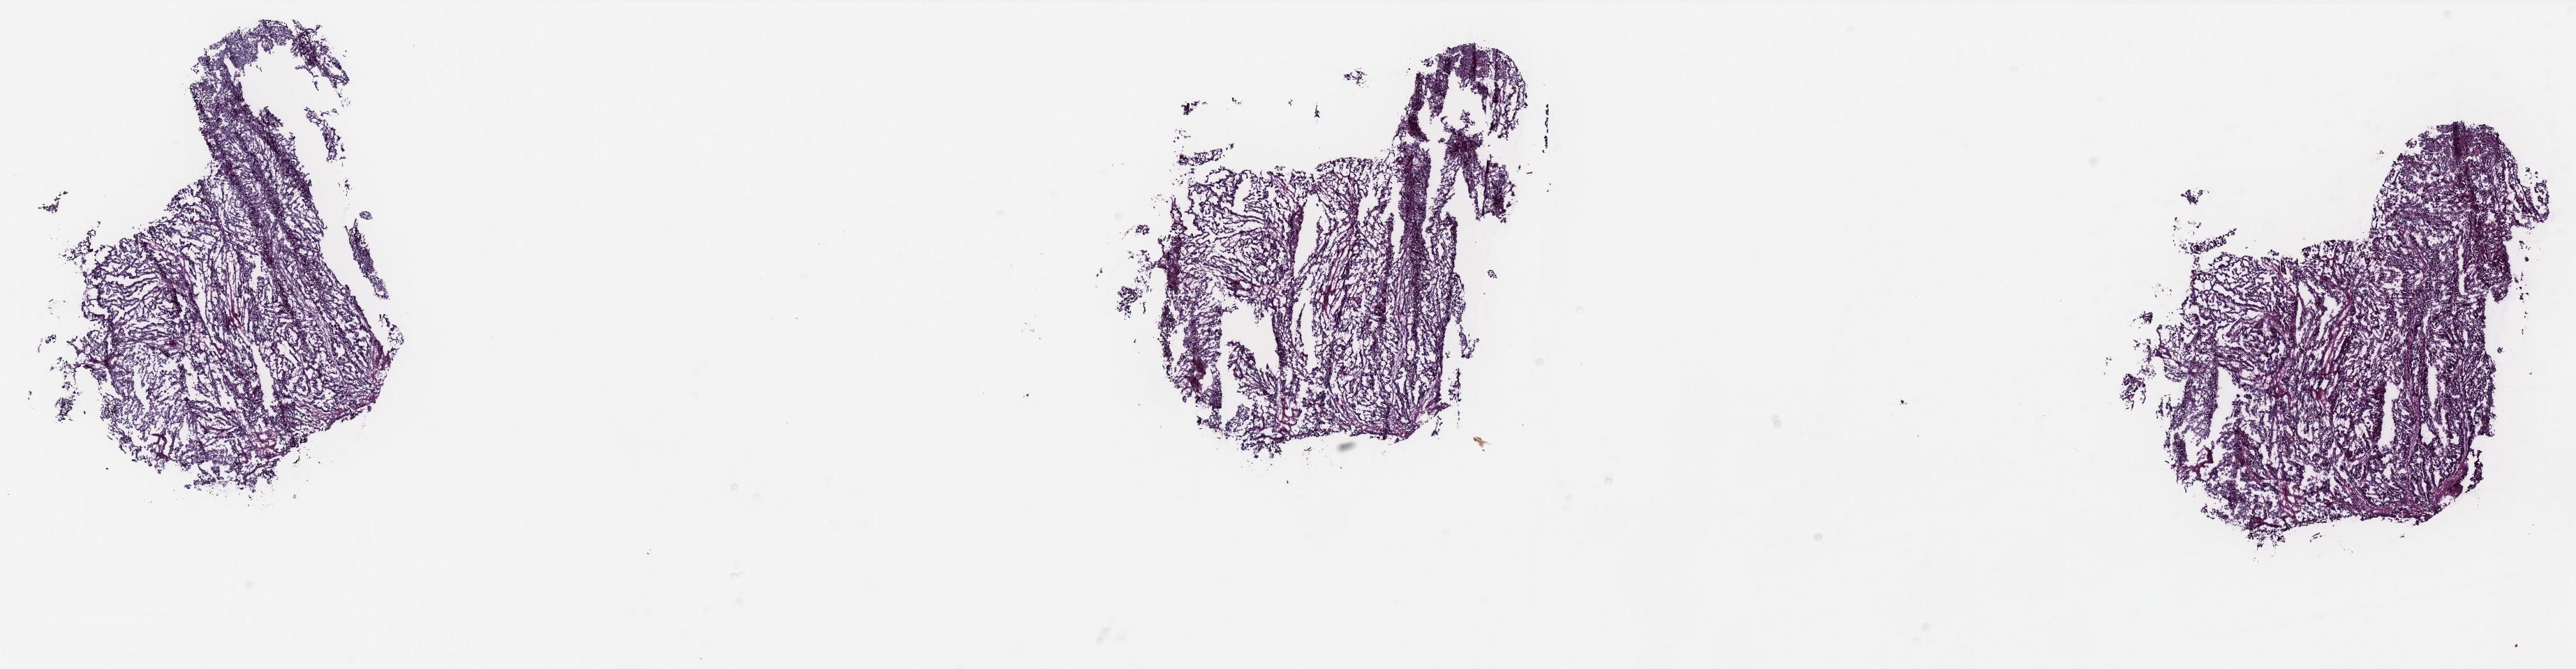
H&E-stained whole-slide image — low-resolution overview of the scanned area, about 29.6 x 7.7 mm (from a 40x scan); frozen section from the bottom of the tissue portion; sample: primary tumour, uterus. Patient: female, age at initial diagnosis 58 years. Histologic grade: G1 (well differentiated). Composition of this section per pathologist review: tumour cells 100%, tumour nuclei 90%, normal cells 0%, stromal cells 0%, necrosis 0%. Infiltration values recorded for this section: lymphocyte infiltration 1%, monocyte infiltration 0%, neutrophil infiltration 0%.
Histologic diagnosis: Endometrioid adenocarcinoma, NOS (endometrium). Lymph nodes positive (case pathology): 0 of 1 examined. FIGO stage: IA.